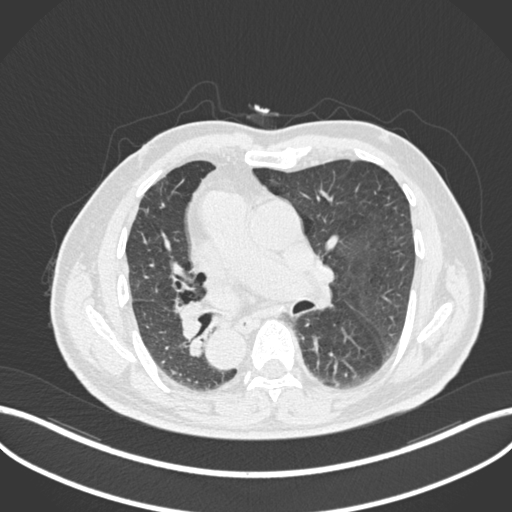
Chest CT, one axial slice. Reconstruction kernel B30f. 120 kVp. Lung window (W 1500 / L -600 HU). 1 mm slice thickness. 512 × 512 image matrix, field of view 400 × 400 mm. Male patient, age 67 years. From the clinical record (not read from this slice): clinical TNM (as recorded): T2a N0 M0.
Structures marked on this image (rectangle marked by the reading radiologist):
- lung tumour (recorded histology: squamous cell carcinoma): bounding box [x1, y1, x2, y2] px = [174, 295, 208, 339]